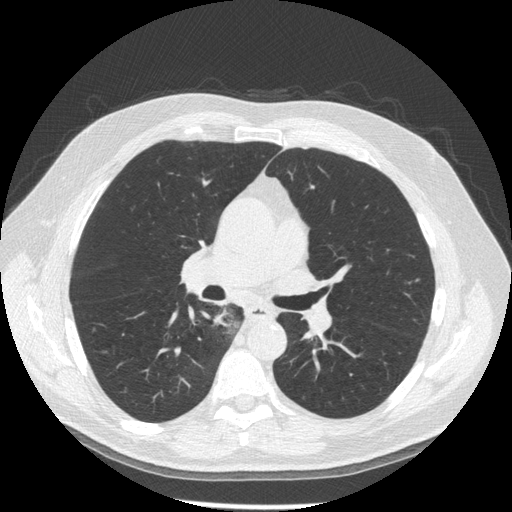
Low-dose screening chest CT, one axial slice. Slice 105 of 181 in the series (ordered by position). Lung window (W 1500 / L -600 HU). 1.25 mm slice thickness. 512 × 512 image matrix.
Outlined on this slice (manually delineated by an expert):
- lesion 1 (tumor, lower lobe of right lung): box from (x=214, y=311) to (x=227, y=326) px